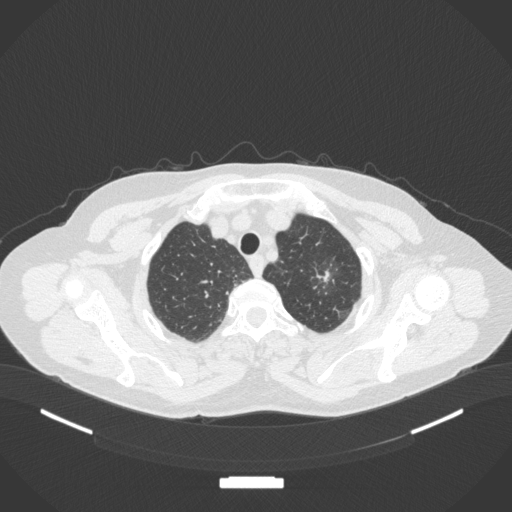
Chest CT, one axial slice; slice 312 of 369 in the series (ordered by position); lung window (W 1500 / L -600 HU); 1 mm slice thickness; 512 × 512 image matrix, field of view 400 × 400 mm. Female patient, age 64 years. From the clinical record (not read from this slice): clinical TNM (as recorded): T1c N0 M0.
Annotated regions visible in this slice (bounding box drawn by a radiologist):
- lung tumour (recorded histology: adenocarcinoma): bounding box [x1, y1, x2, y2] px = [301, 246, 352, 305]